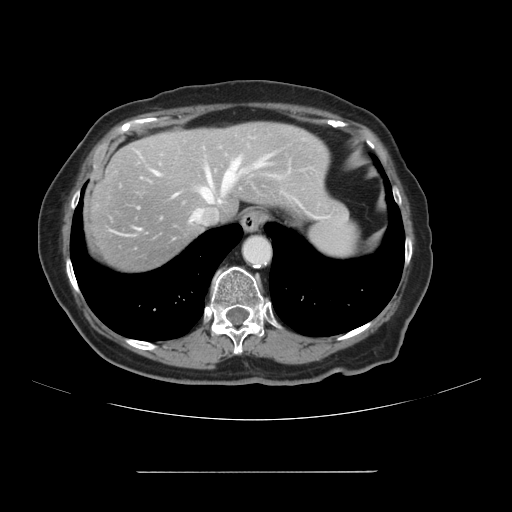
Contrast-enhanced abdominal CT, one axial slice; slice 90 of 111 in the series (ordered by position); intravenous contrast given; soft-tissue window (W 400 / L 40 HU); 2.5 mm slice thickness; 512 × 512 image matrix. Female patient, age 74 years. Case-level facts recorded for this patient, not image findings: diagnosis: colorectal cancer liver metastases, imaged before liver resection; multiple liver metastases: yes; largest metastasis: 1.1 cm.
Structures marked on this image (manually delineated by an expert):
- hepatic veins: bounding box <155,138,306,221> (left, top, right, bottom; pixels)
- liver: <86,122,341,274>
- planned liver remnant (the part of the liver to remain after resection): <171,122,341,218>
- portal vein (with intrahepatic branches): <205,156,269,195>